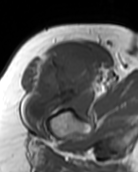
MRI of an extremity soft-tissue mass, one axial slice. Position 77 of 99 along the scan axis. MR volume resampled by the dataset authors to the PET/CT grid (not the native acquisition matrix). 3.27 mm slice thickness. 138 × 172 image matrix. Female patient. From the clinical record (not read from this slice): histological type: pleiomorphic undifferentiated sarcoma; grade: high; site of the primary tumour: right quadricep.
Annotated regions visible in this slice (expert contour drawn on MRI and transferred to this co-registered scan by the dataset authors):
- gross tumour volume including surrounding oedema: box from (x=25, y=48) to (x=95, y=120) px
- gross tumour volume (mass): (x=25, y=48)–(x=95, y=120)